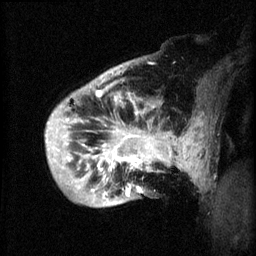
Breast MRI (dynamic contrast-enhanced), one sagittal slice. 3 images stored at this slice position (order not interpretable as contrast timing). 1.5 T. TE 4.2 ms, TR 8.2 ms. 2 mm slice thickness. 256 × 256 image matrix, field of view 200 × 200 mm. Patient: female, 50 years.
Outlined on this slice (semi-automatic segmentation, software-assisted and operator-edited):
- analysis volume of interest (the breast-tissue region the enhancement analysis was run in; not a lesion): box from (x=46, y=72) to (x=173, y=207) px
- tumour enhancement mask (voxels above the 70 % enhancement threshold inside the analysis volume of interest): (x=46, y=86)–(x=173, y=197)